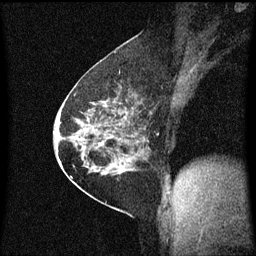
Breast MRI (dynamic contrast-enhanced), one sagittal slice; position 35 of 60 along the scan axis; dynamic contrast-enhanced series, image 2 of 3 at this slice position (ordered by acquisition); 1.5 T; TE 4.2 ms, TR 8.4 ms; 2 mm slice thickness; 256 × 256 image matrix. Female patient, age 60 years.
Structures marked on this image (semi-automatically segmented with operator editing):
- analysis volume of interest (the breast-tissue region the enhancement analysis was run in; not a lesion): box from (x=69, y=66) to (x=148, y=193) px
- tumour enhancement mask (voxels above the 70 % enhancement threshold inside the analysis volume of interest): (x=70, y=82)–(x=145, y=175)